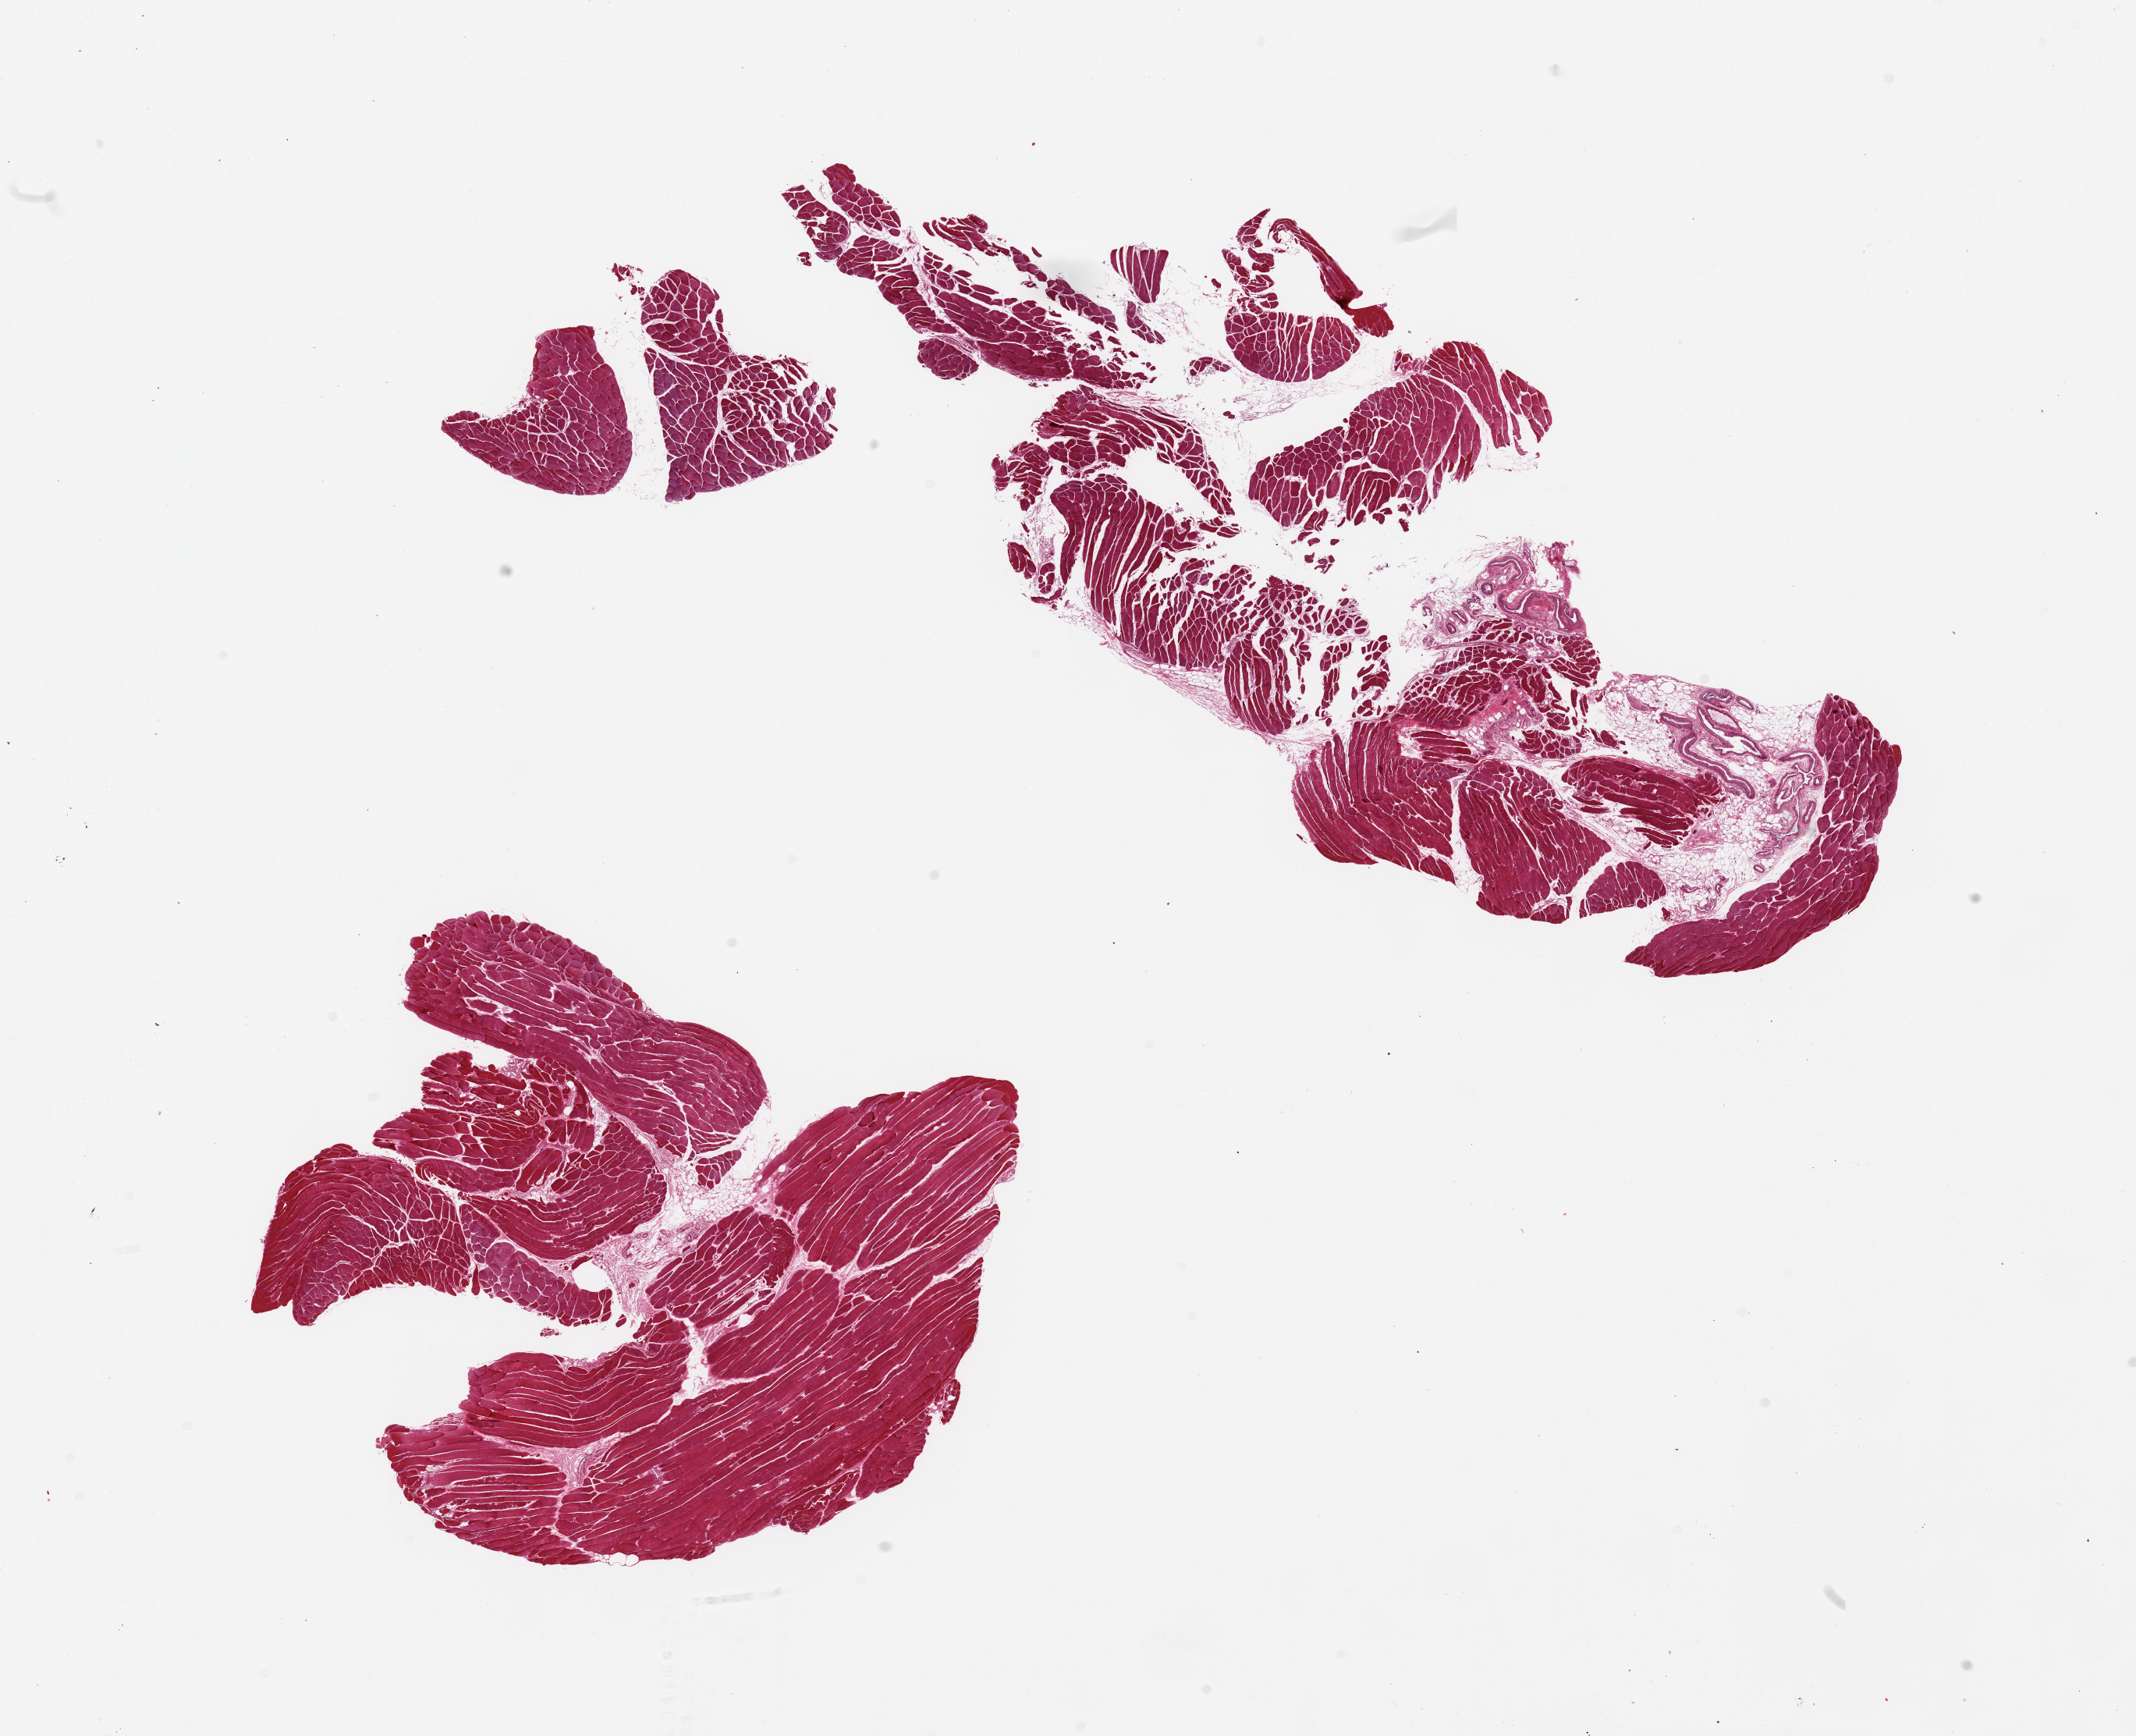
Digitized haematoxylin and eosin-stained section — a low-resolution overview of the entire scanned area, about 21.7 x 17.6 mm, PAXgene-fixed, paraffin-embedded tissue, section of skeletal muscle (target tissue), donor tissue sample. Donor sex: female.
- reviewer comment on this tissue sample: 2 pieces, 1 fragmented